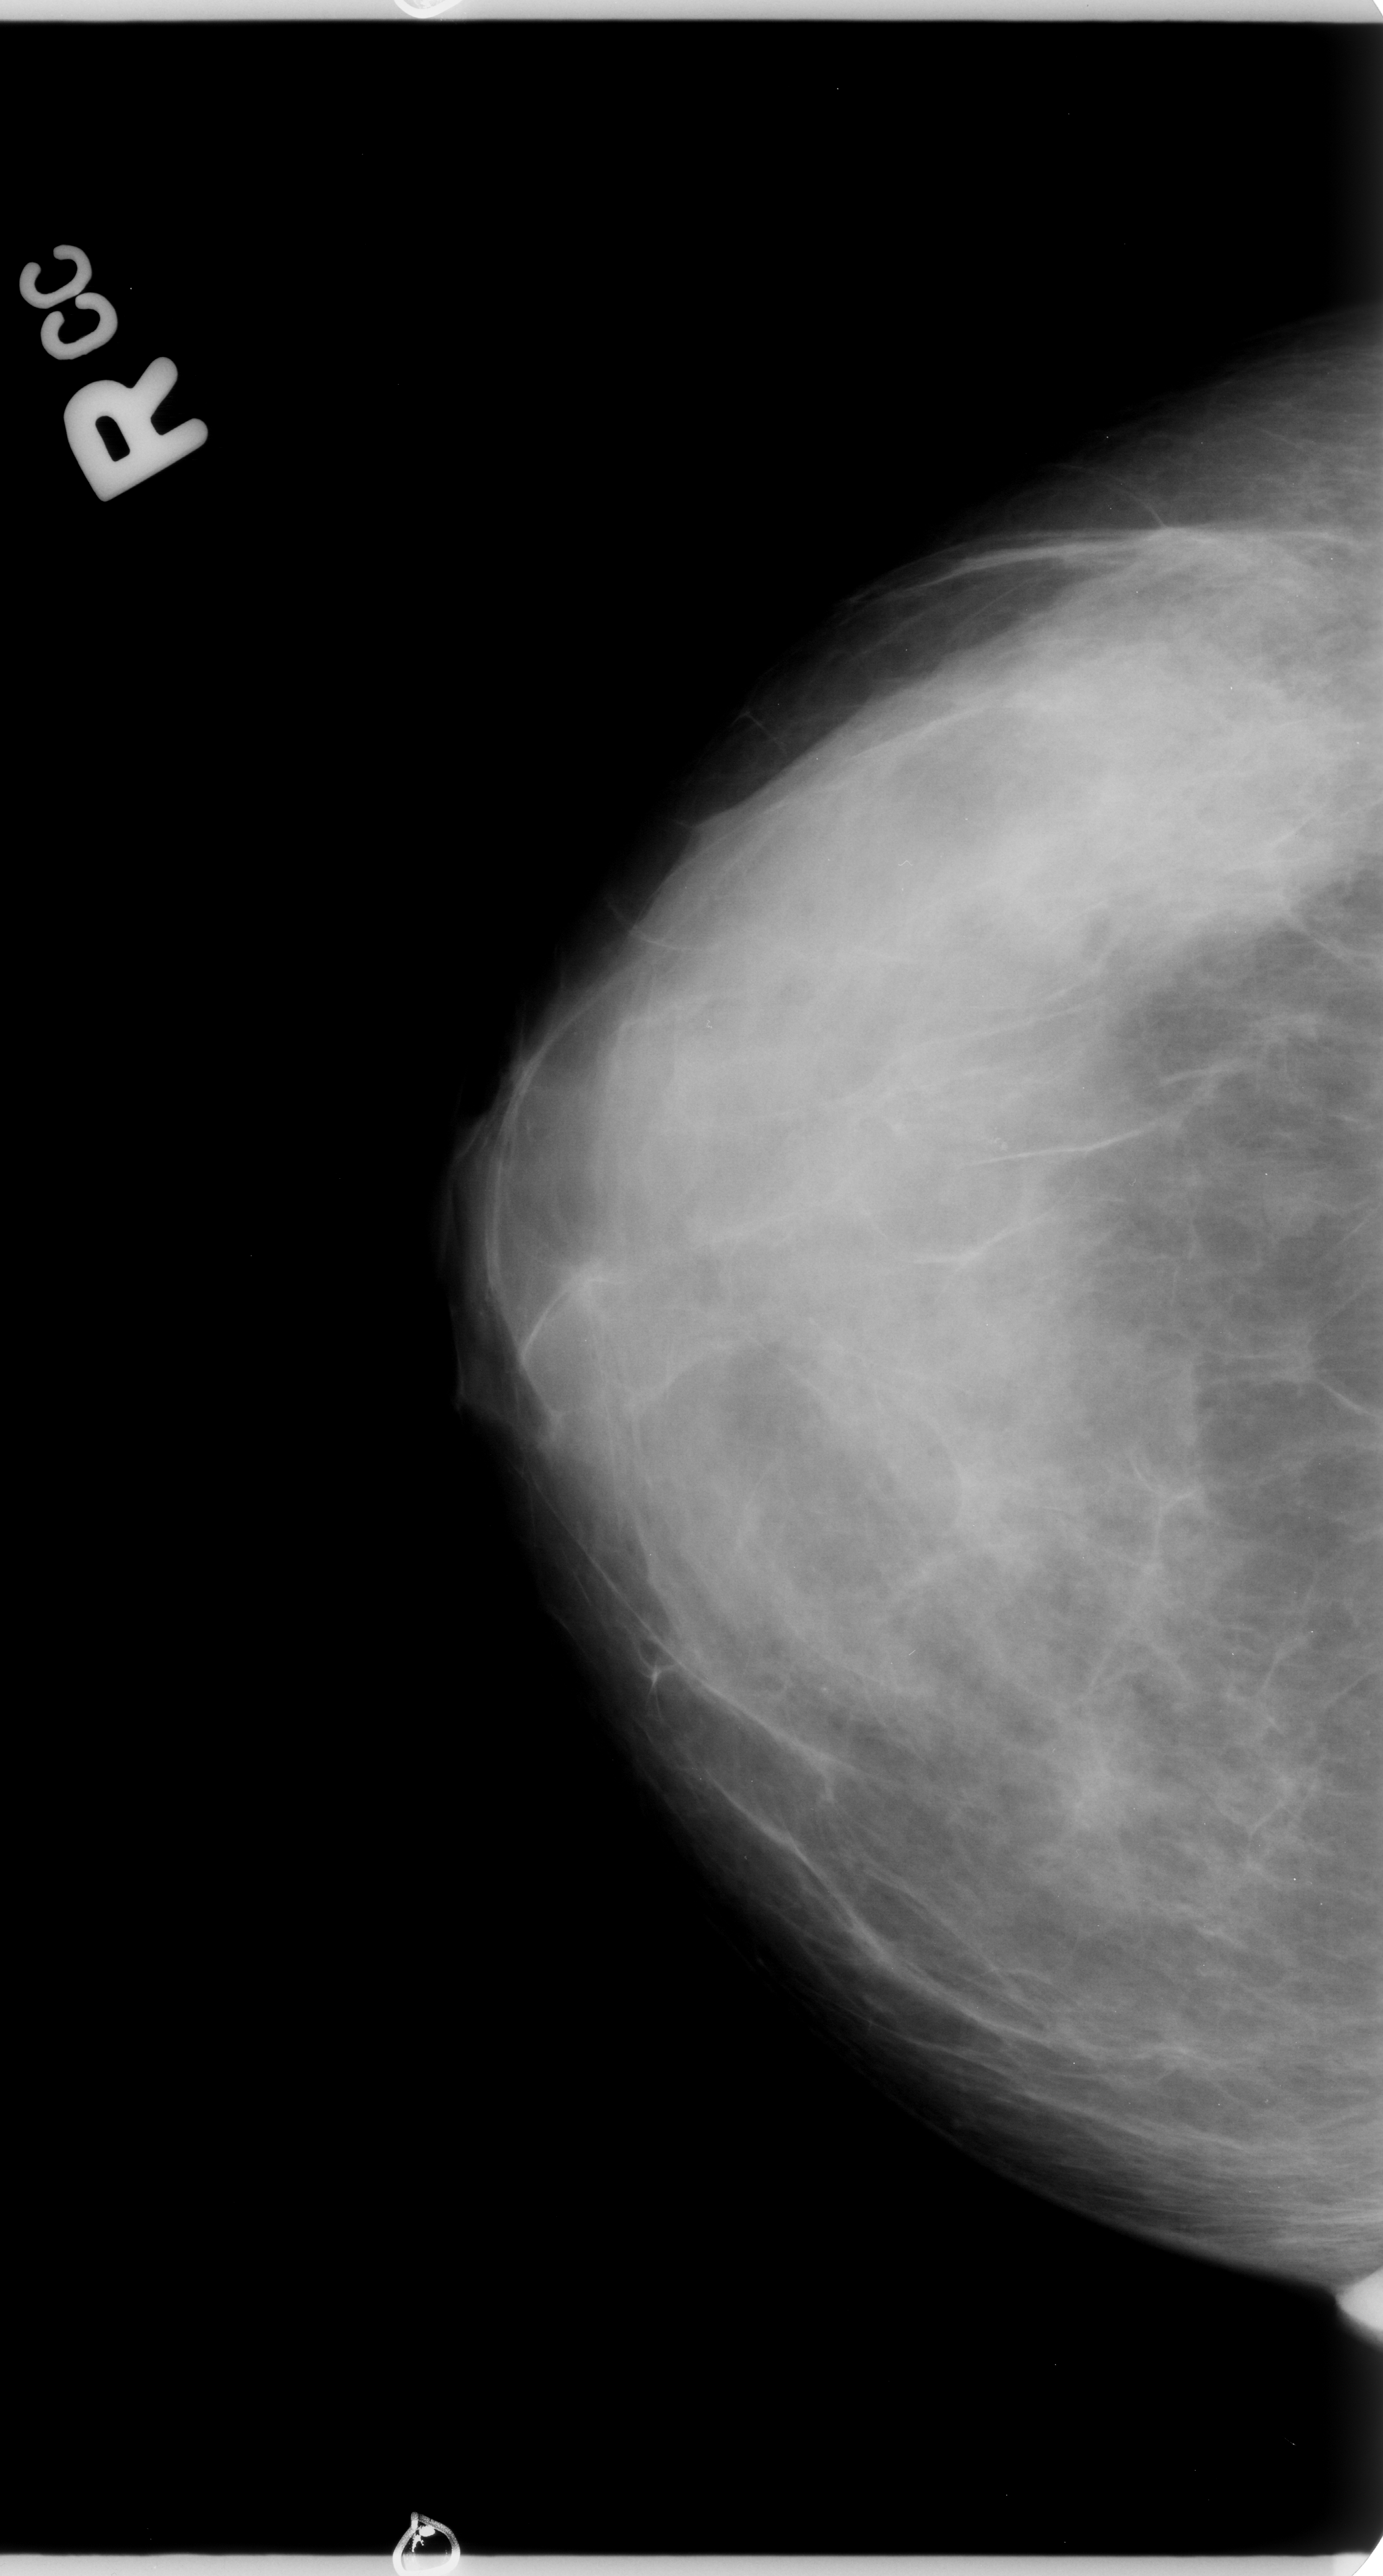
Digitized screen-film mammogram; right breast; CC view; breast composition: extremely dense (BI-RADS density category 4 of 4).
Marked abnormality: calcifications, morphology pleomorphic, distribution clustered; BI-RADS assessment category 4; pathology (as recorded): benign.